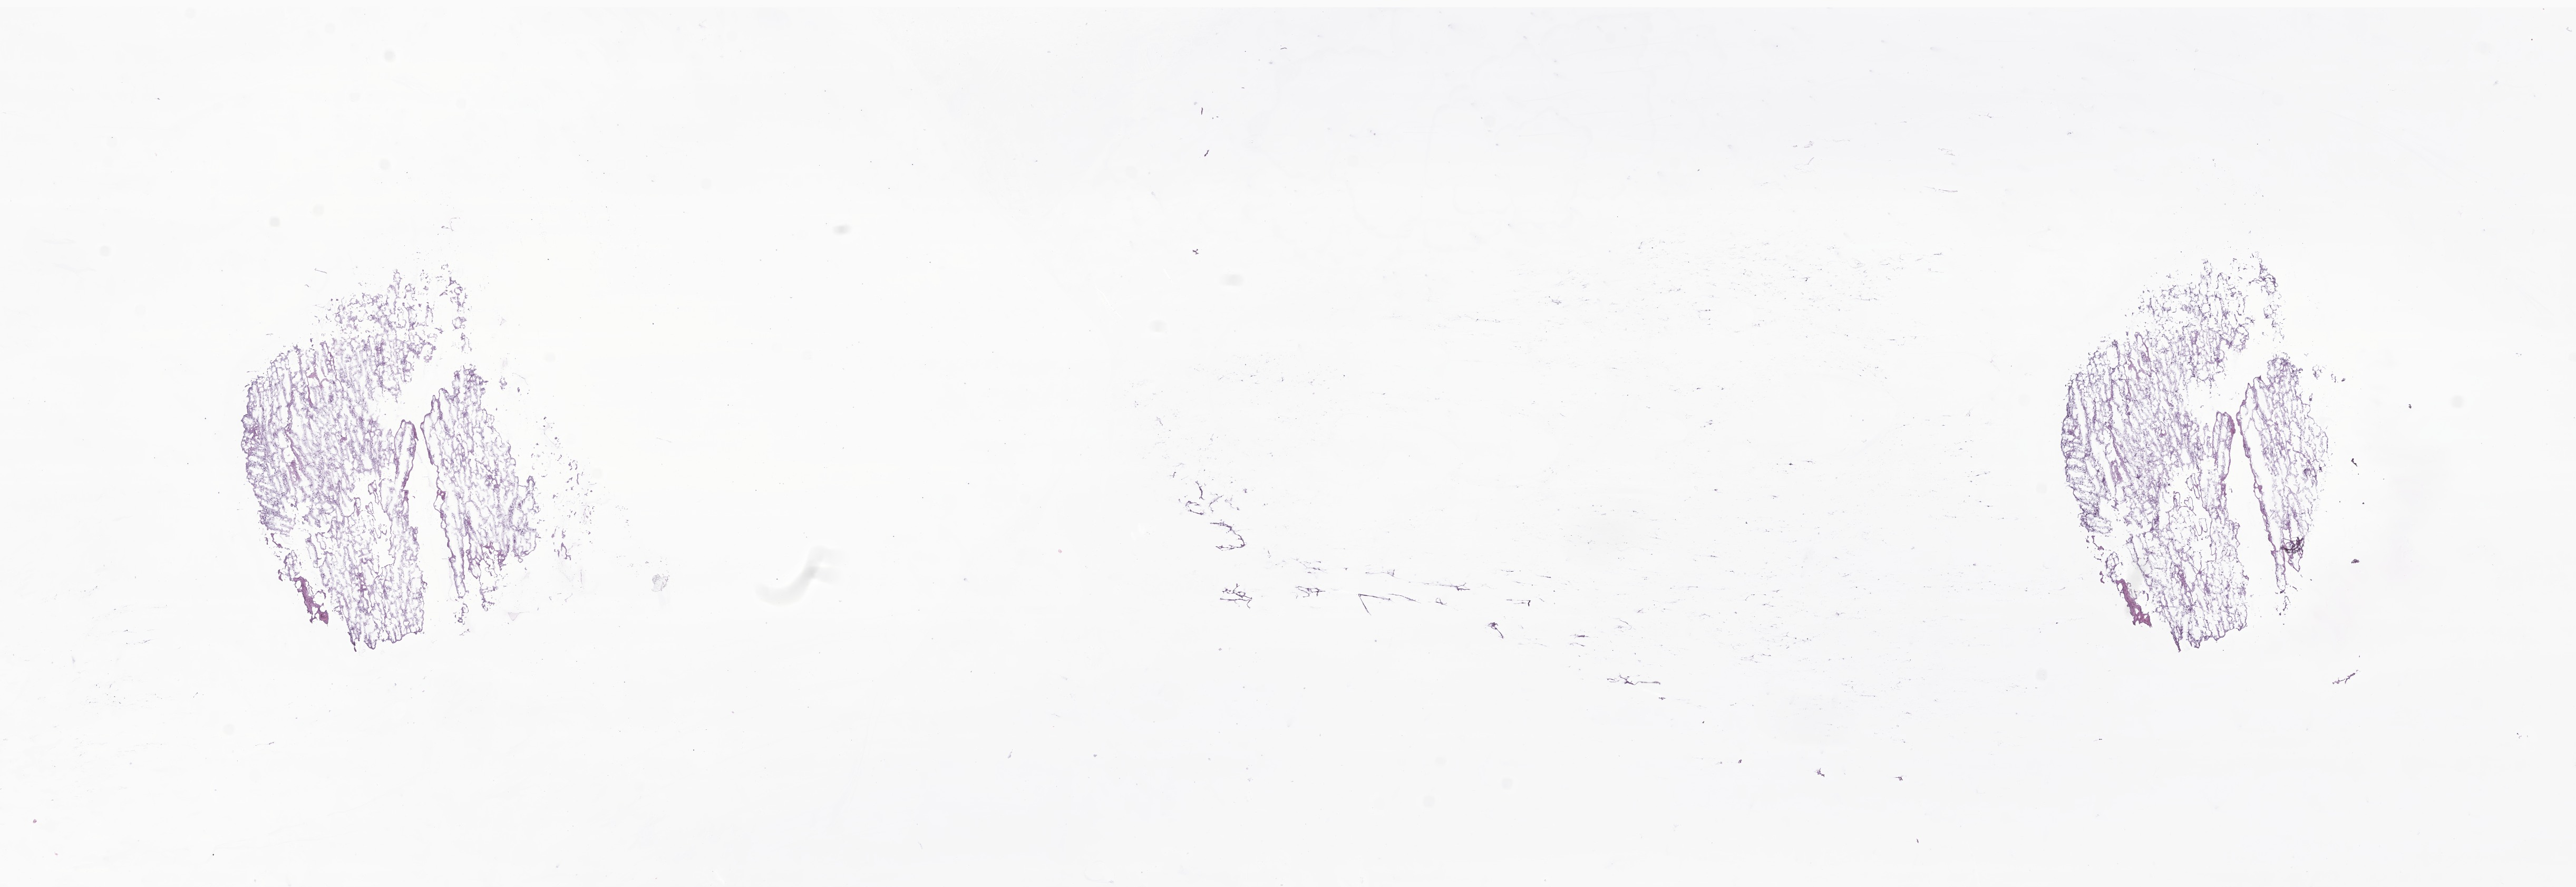
Whole-slide image, H&E stain of tumor tissue from the brain stem — low-resolution overview of the scanned area, about 20.6 x 7.1 mm; frozen section. Patient: male, age 62 months (5 years 2 months).
Diagnosis (ICD-O-3 morphology term): Glioma, malignant.